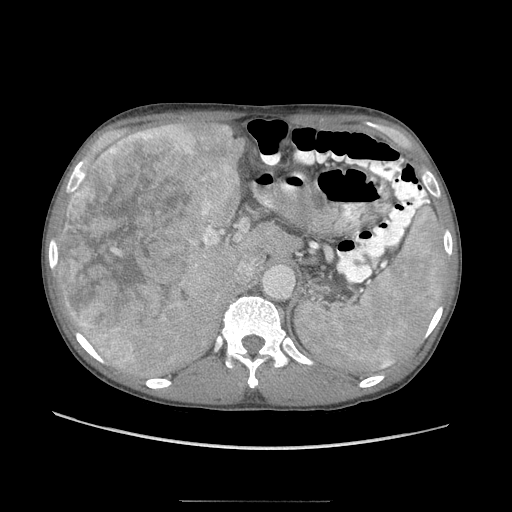
Contrast-enhanced abdominal CT (liver protocol), one axial slice; slice 62 of 103 in the series (ordered by position); reconstruction kernel STANDARD; 120 kVp; soft-tissue window (W 400 / L 40 HU); 2.5 mm slice thickness; 512 × 512 image matrix, field of view 380 × 380 mm. From the clinical record (not read from this slice): diagnosis: hepatocellular carcinoma (patient treated with transarterial chemoembolisation; whether this scan precedes or follows treatment is not stated here); TNM stage (as recorded): Stage-IIIA; Child-Pugh class: A; tumour nodularity: multinodular.
Structures marked on this image (semi-automatically segmented with operator editing):
- liver parenchyma outside the tumour (the mass and vessels are separate outlines, so this box may not span the whole liver): bounding box (x1, y1, x2, y2) in pixels: (56, 114, 296, 376)
- mass: (57, 122, 238, 369)
- liver vessels: (217, 224, 263, 272)